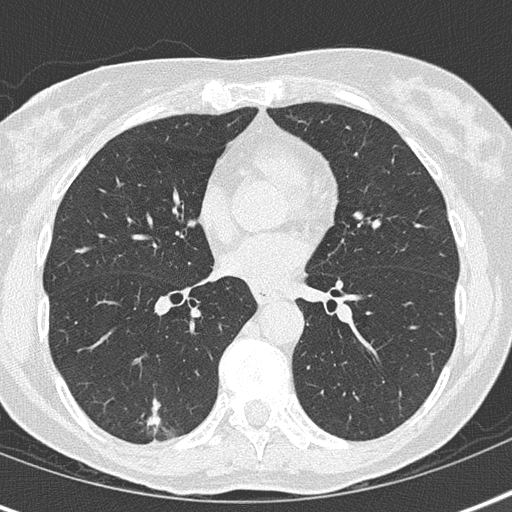
Axial slice from a low-dose chest CT screening exam, first (baseline) screen, lung window (W 1500 / L -600 HU), 2 mm slice thickness, lung (sharp) reconstruction kernel (B50f), 512 × 512 image matrix. Female, age 69 years at enrolment. Current smoker at enrolment.
• Lesion marked by an expert reader, bounding box [x1, y1, x2, y2] px = [118, 395, 181, 453].
• The screening reader recorded 2 non-calcified nodules or masses ≥4 mm on this exam (right lower lobe, left lower lobe); which of them this box marks is not recorded.